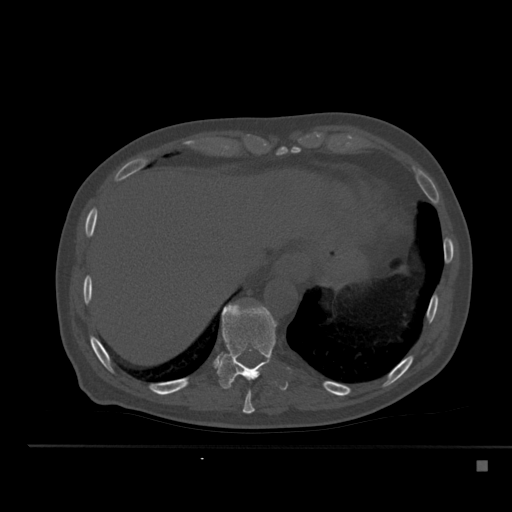
CT including the spine, one axial slice; slice 270 of 517 in the series (ordered by position); reconstruction kernel Br40s; bone window (W 1800 / L 400 HU); 1.5 mm slice thickness; 512 × 512 image matrix, field of view 408 × 408 mm. Patient: male, 70 years. From the clinical record (not read from this slice): primary cancer: renal; vertebrae with lytic lesions (as recorded): T4, T6, T10, T12, L3, L4, L5.
Outlined on this slice (semi-automatic segmentation, software-assisted and operator-edited):
- T10 vertebra: bounding box <217,304,277,389> (left, top, right, bottom; pixels)
- T9 vertebra: <242,390,255,414>